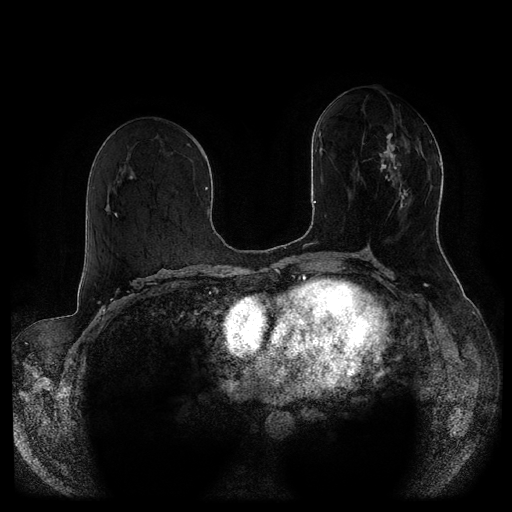
Breast MRI (dynamic contrast-enhanced, multi-phase), one axial slice; position 48 of 116 along the scan axis; dynamic contrast-enhanced series, time point 2 of 5 at this slice position (early post-contrast); 1.5 T; TE 2.6 ms, TR 5.3 ms; 2 mm slice thickness; 512 × 512 image matrix, field of view 370 × 370 mm. Female patient, age 51 years.
Outlined on this slice (semi-automatic segmentation, software-assisted and operator-edited):
- breast lesion (labelled 'tumour' in the annotation; benign lesions carry a separate 'benign' label): bounding box <369,133,411,215> (left, top, right, bottom; pixels)